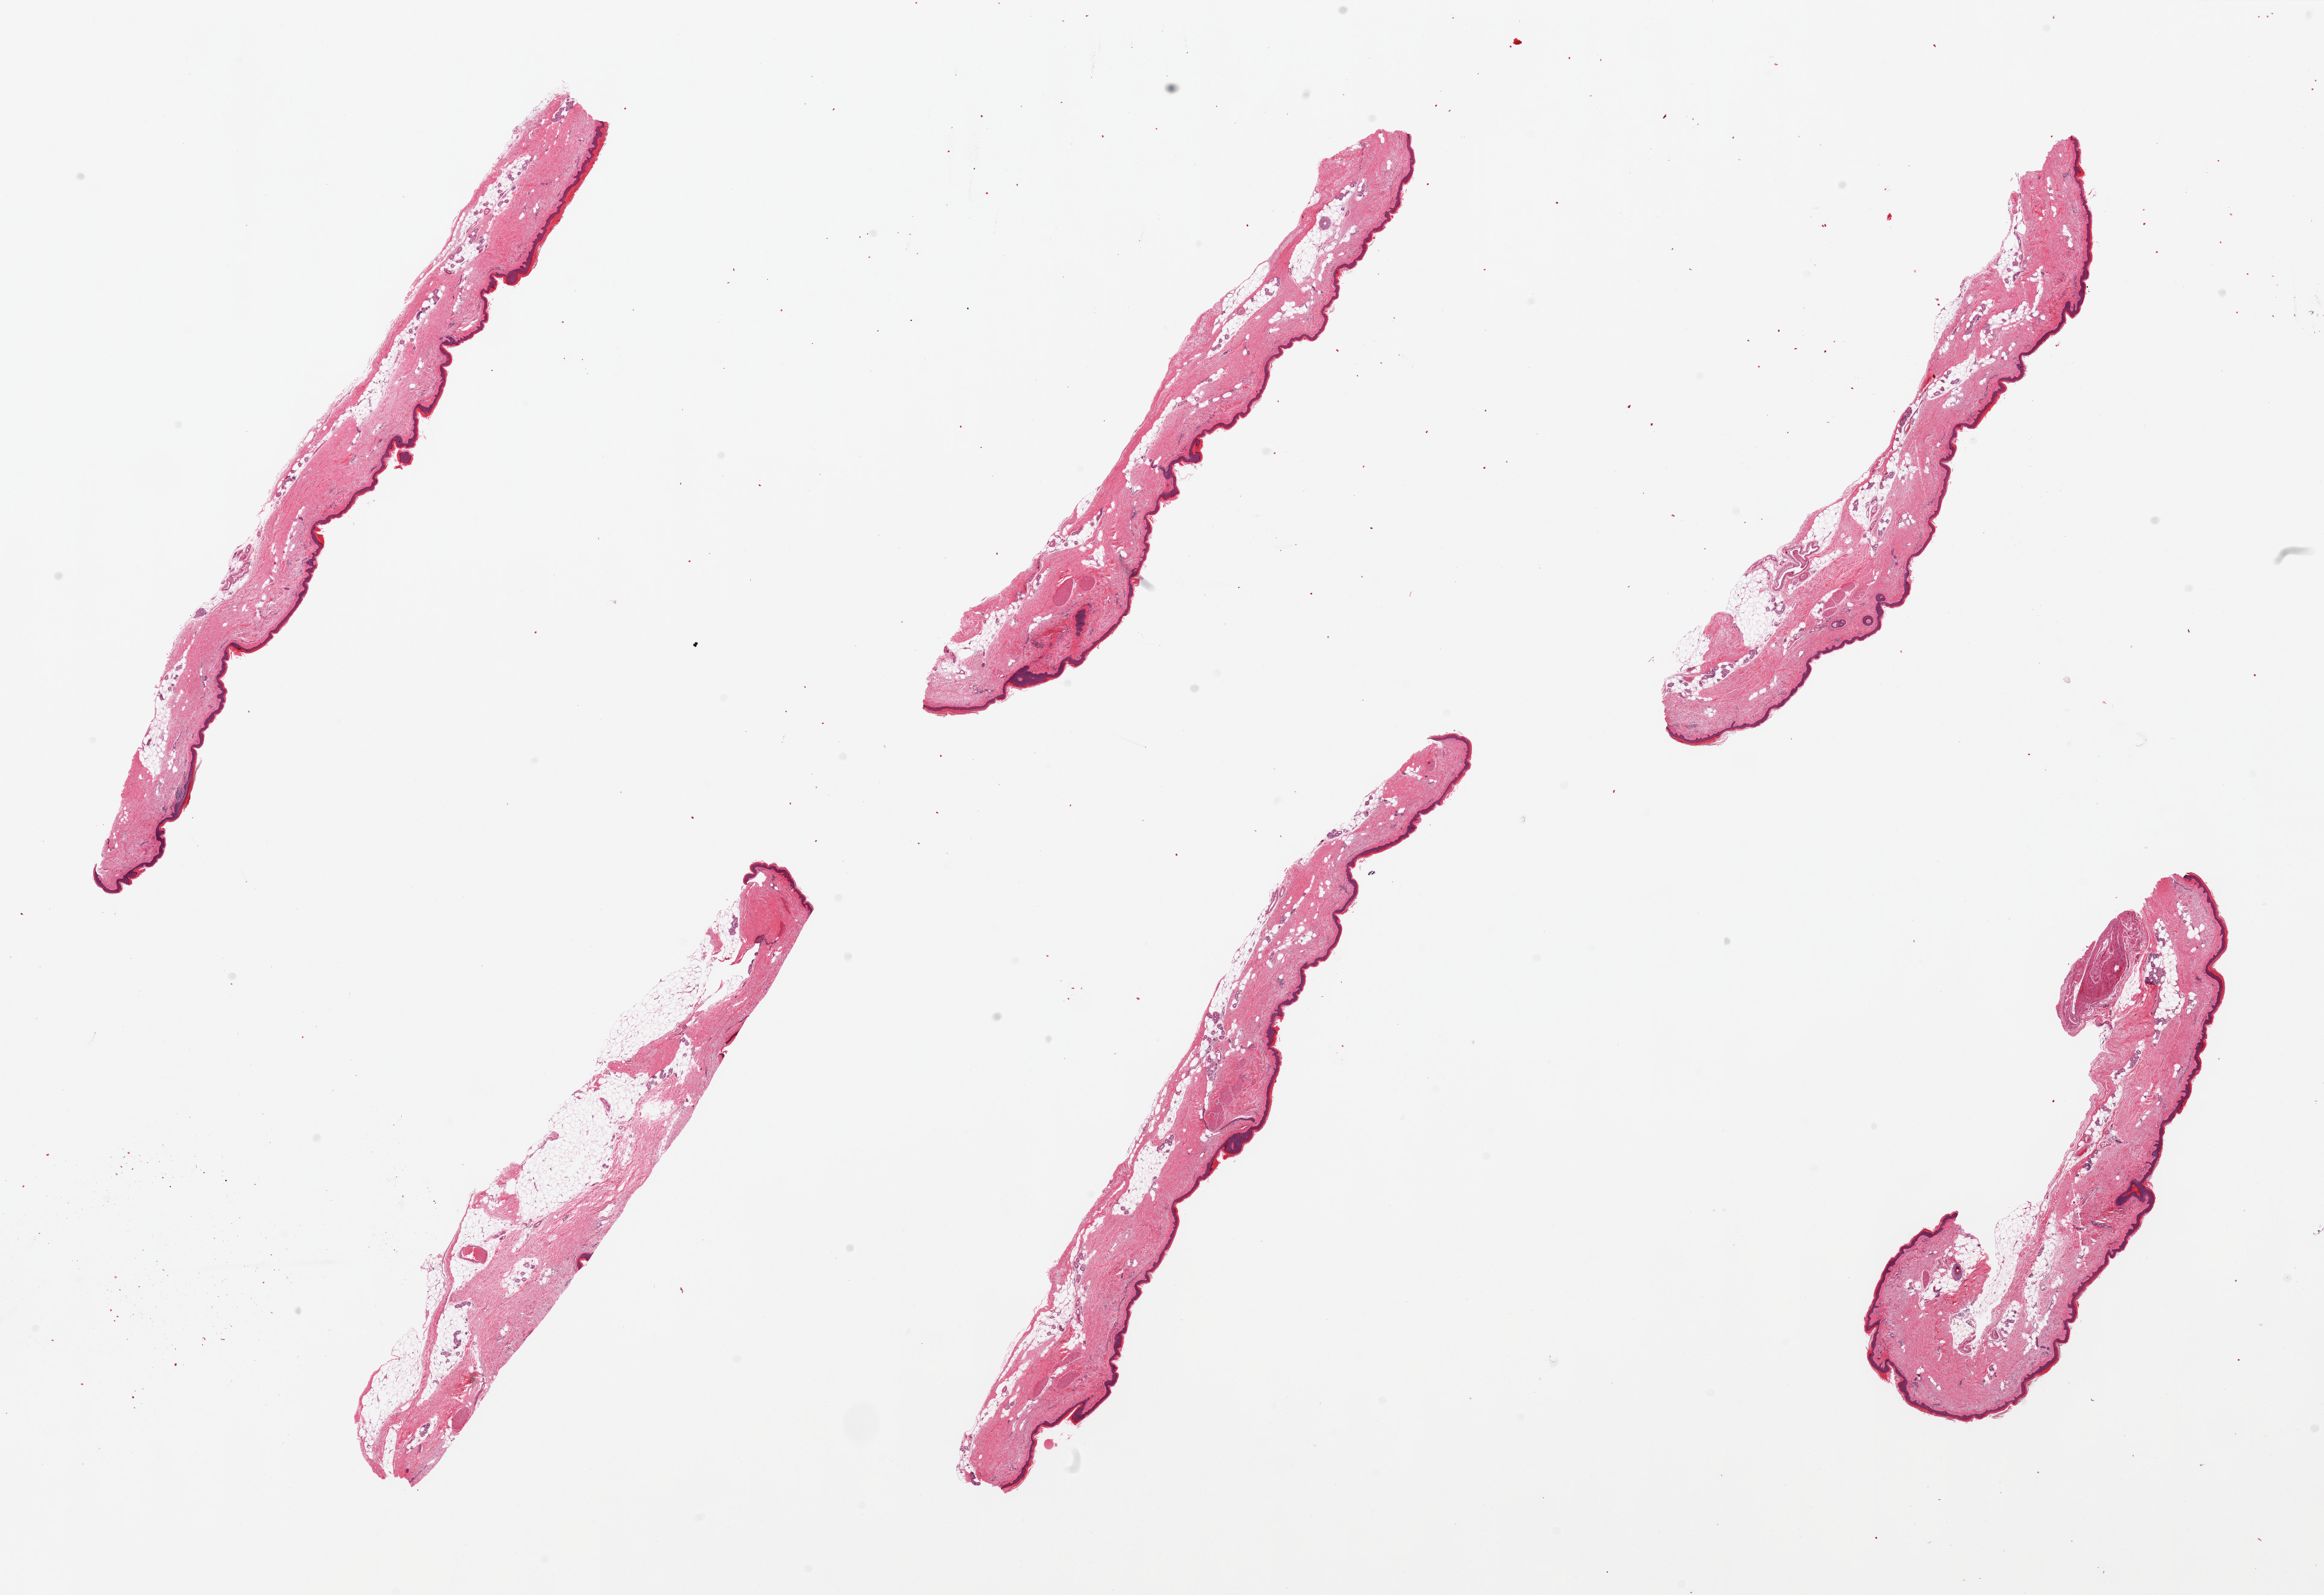
Hematoxylin and eosin (H&E) whole-slide image — a low-resolution overview of the entire scanned area, about 30.5 x 20.9 mm (from a 20x scan); PAXgene-fixed, paraffin-embedded tissue; sampled site (target tissue): skin of lower leg; tissue donor sample. Donor: female.
- review note (as recorded): 6 pieces, squamous epithelium is 40-50 microns